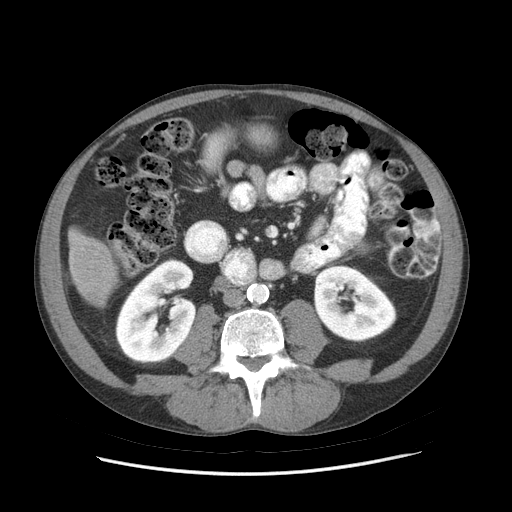
Contrast-enhanced abdominal CT (liver protocol), one axial slice. Position 14 of 89 along the scan axis. Soft-tissue window (W 400 / L 40 HU). 512 × 512 image matrix, field of view 380 × 380 mm. Case-level facts recorded for this patient, not image findings: diagnosis: hepatocellular carcinoma (patient treated with transarterial chemoembolisation; whether this scan precedes or follows treatment is not stated here); TNM stage (as recorded): Stage-IIIB; Child-Pugh class: A.
Outlined on this slice (semi-automatic segmentation, software-assisted and operator-edited):
- liver parenchyma outside the tumour (the mass and vessels are separate outlines, so this box may not span the whole liver): bounding box <68,227,116,304> (left, top, right, bottom; pixels)